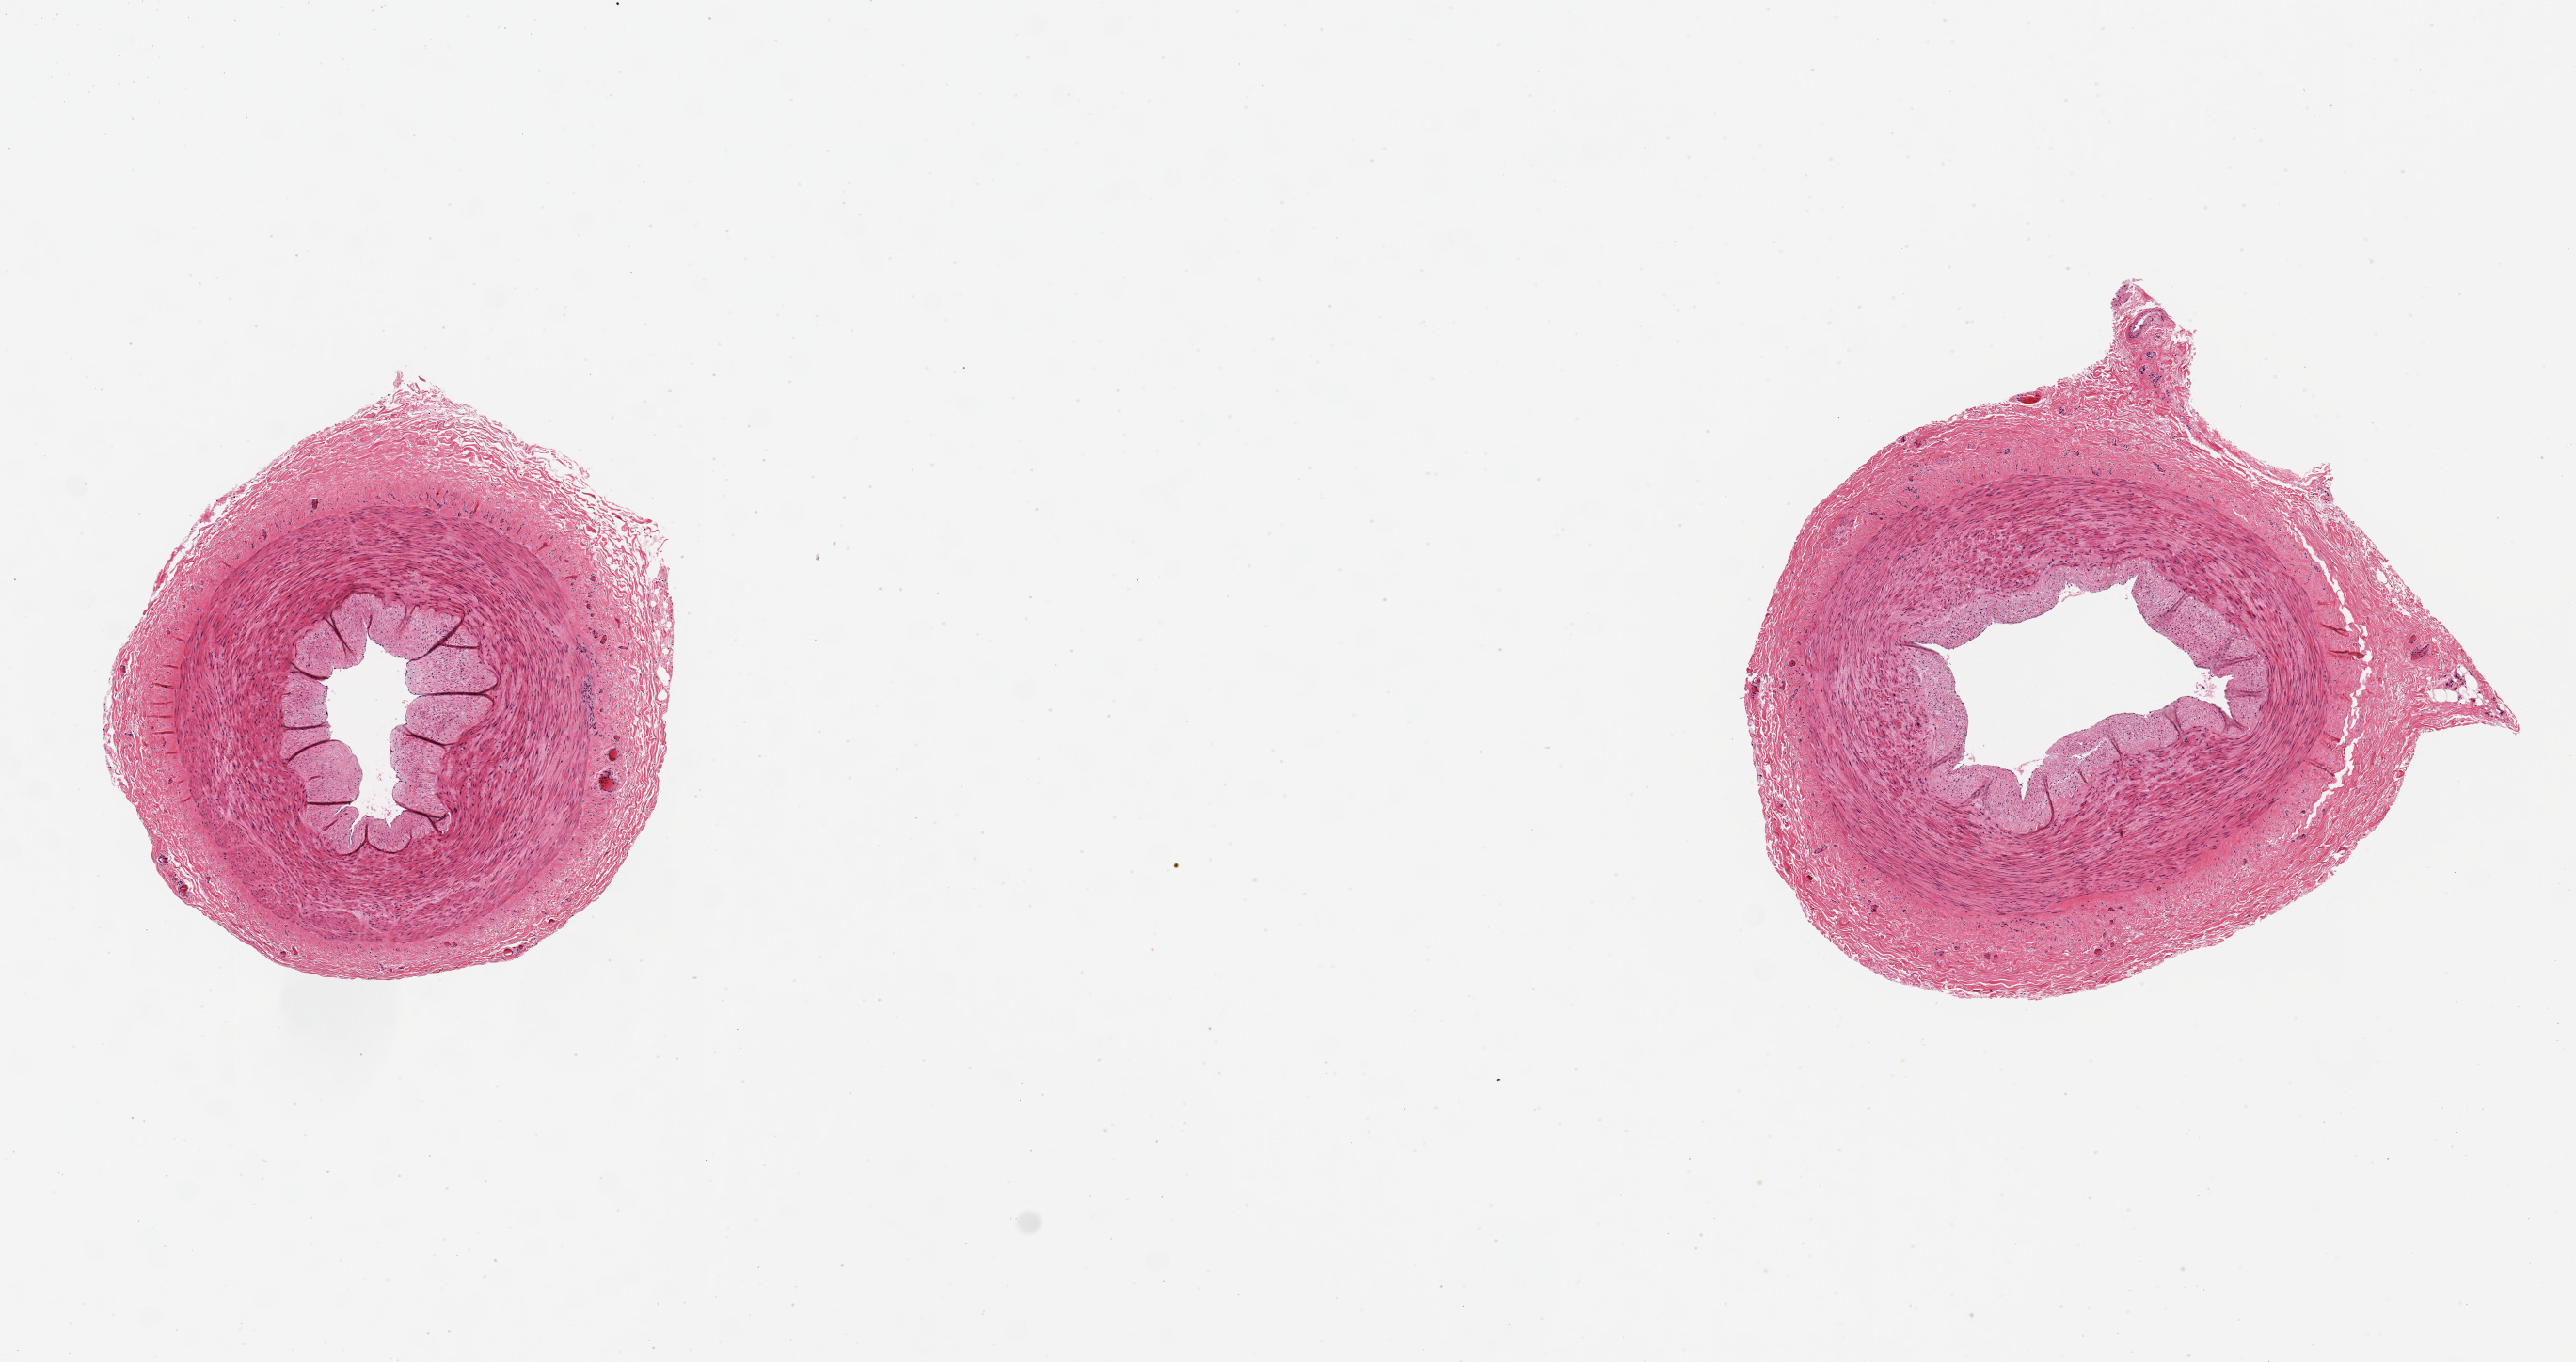
H&E whole-slide image, low-resolution overview of the scanned area, about 10.8 x 5.7 mm, PAXgene-fixed paraffin-embedded (PFPE) section, target tissue: tibial artery, donor tissue sample. Donor sex: male.
Review note (as recorded): 2 ~2.5mm d. aliquots; excellent clean specimens.